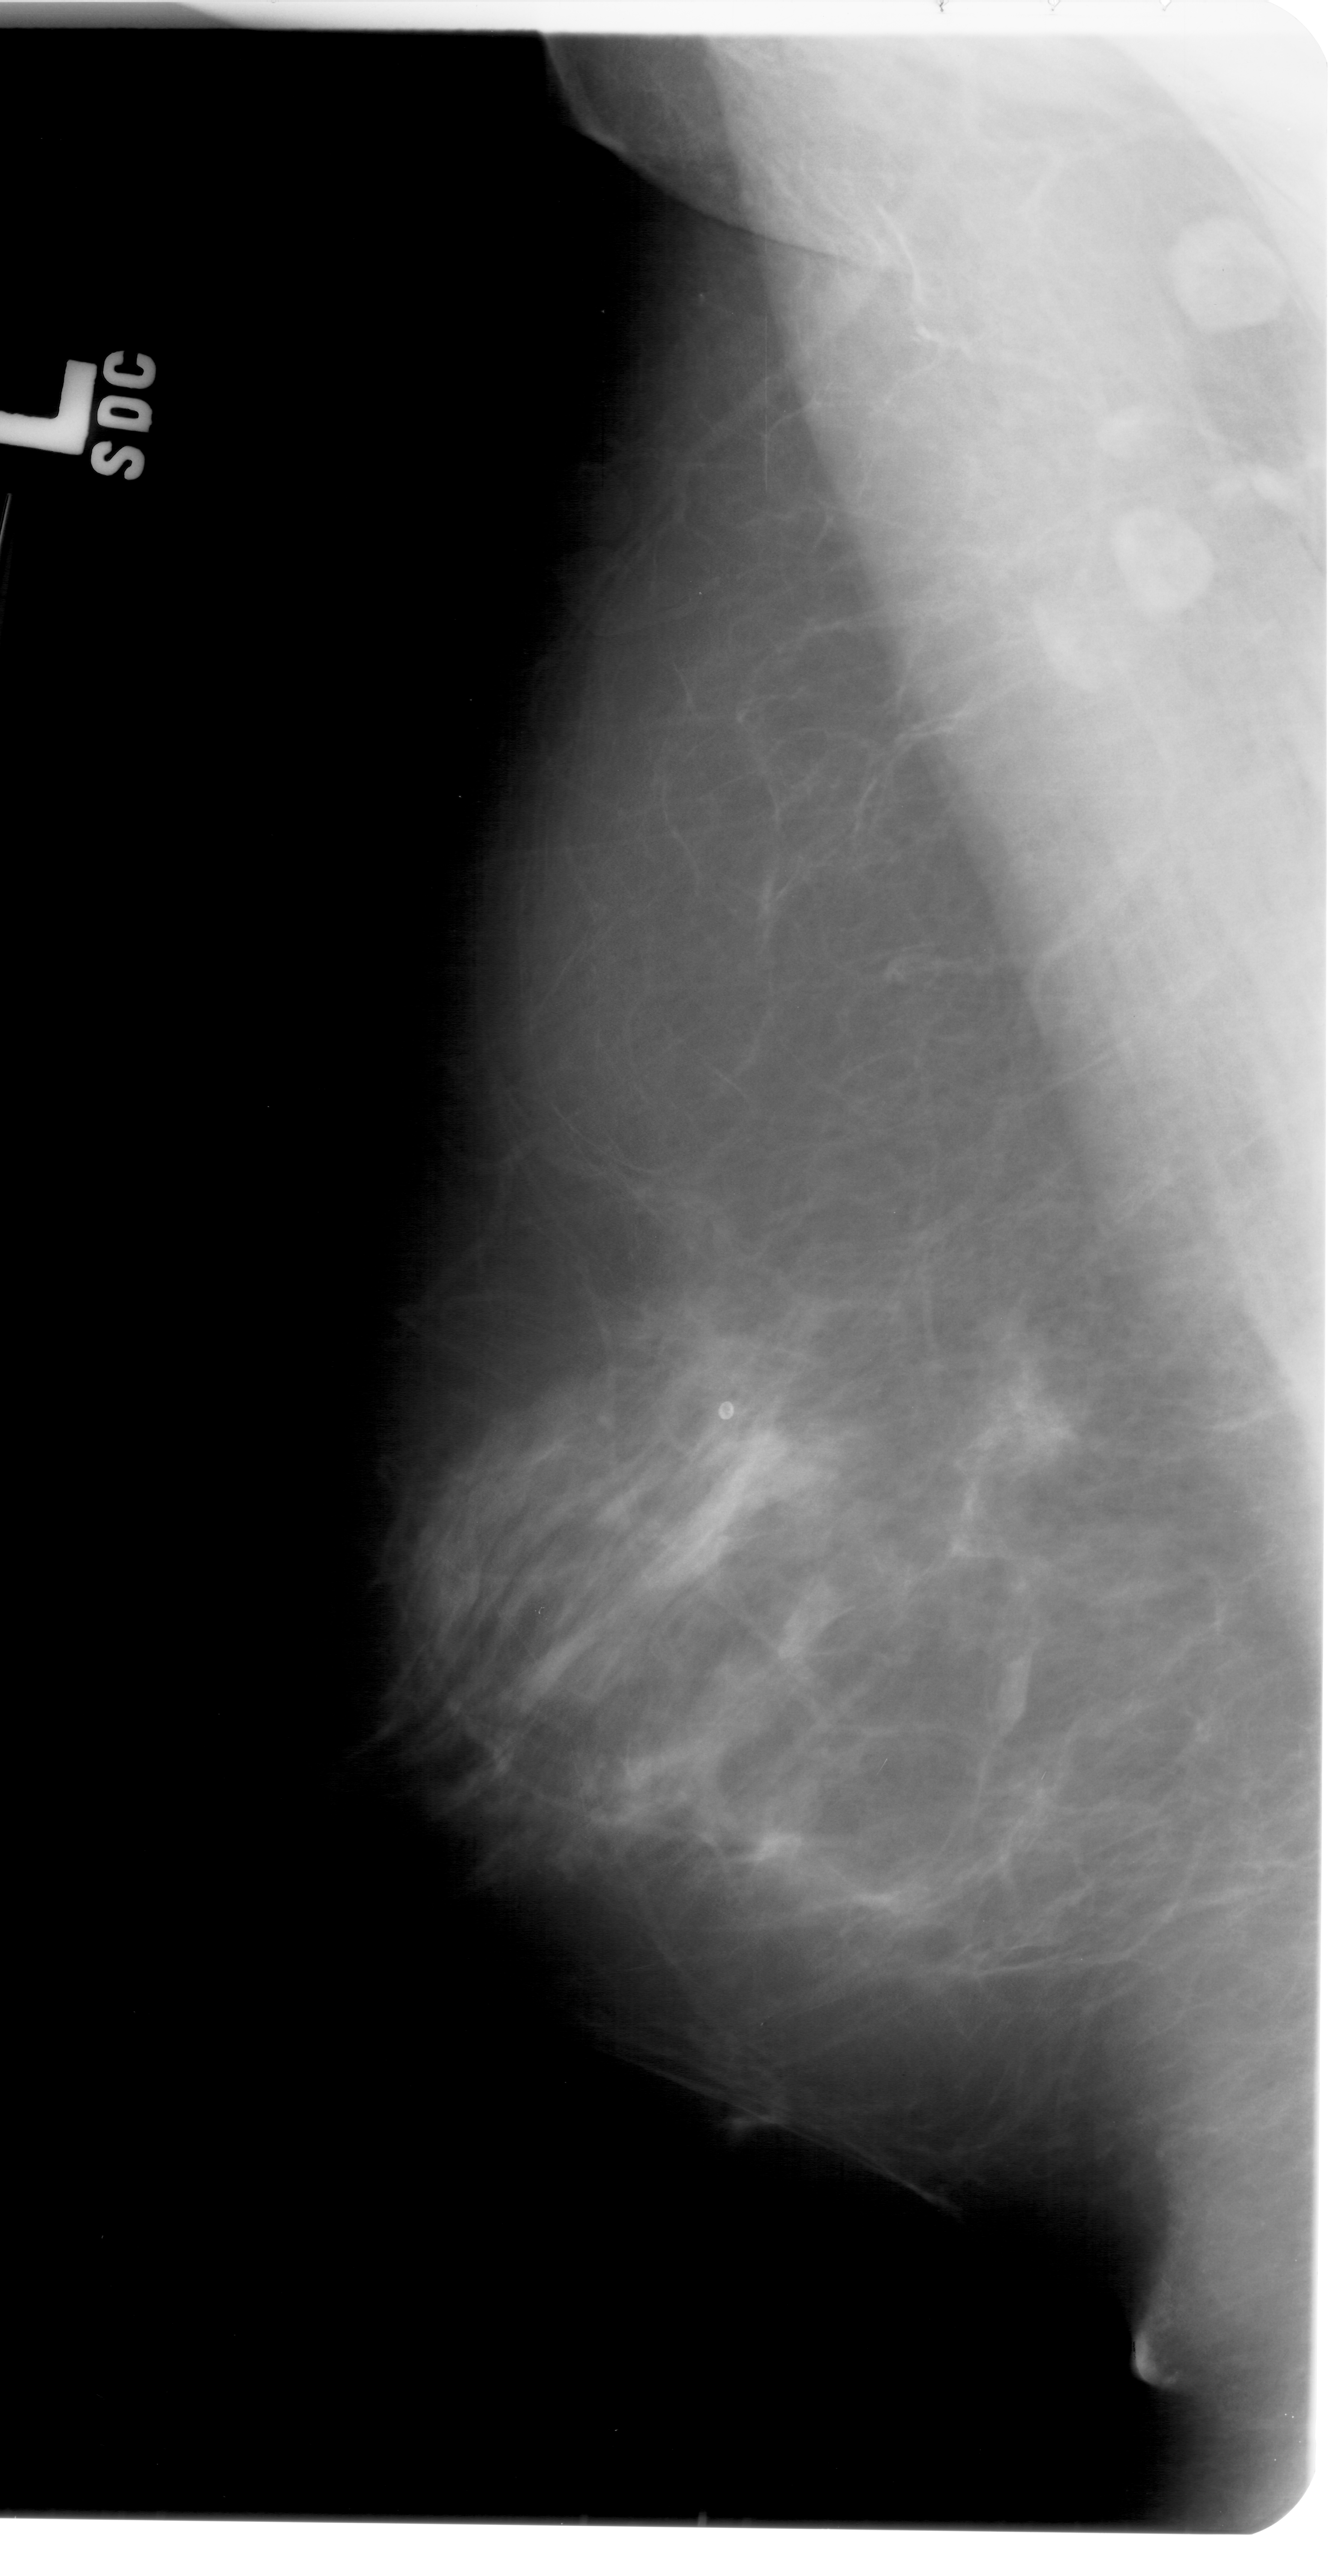
Digitized screen-film mammogram; left breast; MLO view; 1328 × 2576 image matrix.
Expert-marked regions of interest on this image (one box per marked abnormality):
- mass, shape irregular, margins ill defined; BI-RADS assessment category 4; subtlety rating 3 on a 1 (subtle) to 5 (obvious) scale; pathology result (as recorded, not read from the image): benign: bounding box (x1, y1, x2, y2) in pixels: (960, 1322, 1095, 1483)